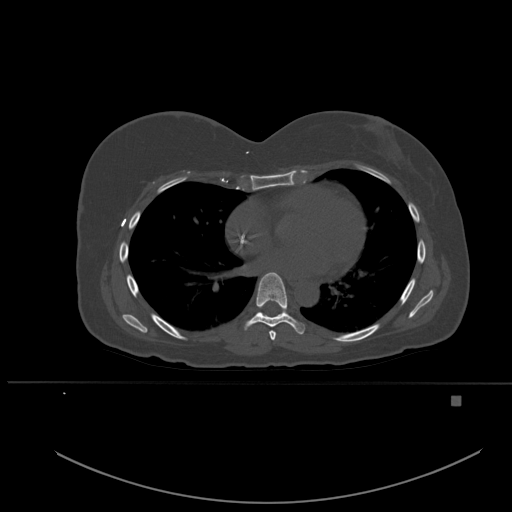
CT including the spine, one axial slice. Slice 336 of 651 in the series (ordered by position). Bone window (W 1800 / L 400 HU). 1.5 mm slice thickness. 512 × 512 image matrix, field of view 443 × 443 mm. Patient: female, 49 years. Case-level facts recorded for this patient, not image findings: primary cancer: breast; vertebrae with lytic lesions (as recorded): L3, T12, L4.
Annotated regions visible in this slice (semi-automatic segmentation, software-assisted and operator-edited):
- T6 vertebra: box from (x=269, y=331) to (x=276, y=341) px
- T7 vertebra: (x=245, y=272)–(x=305, y=335)